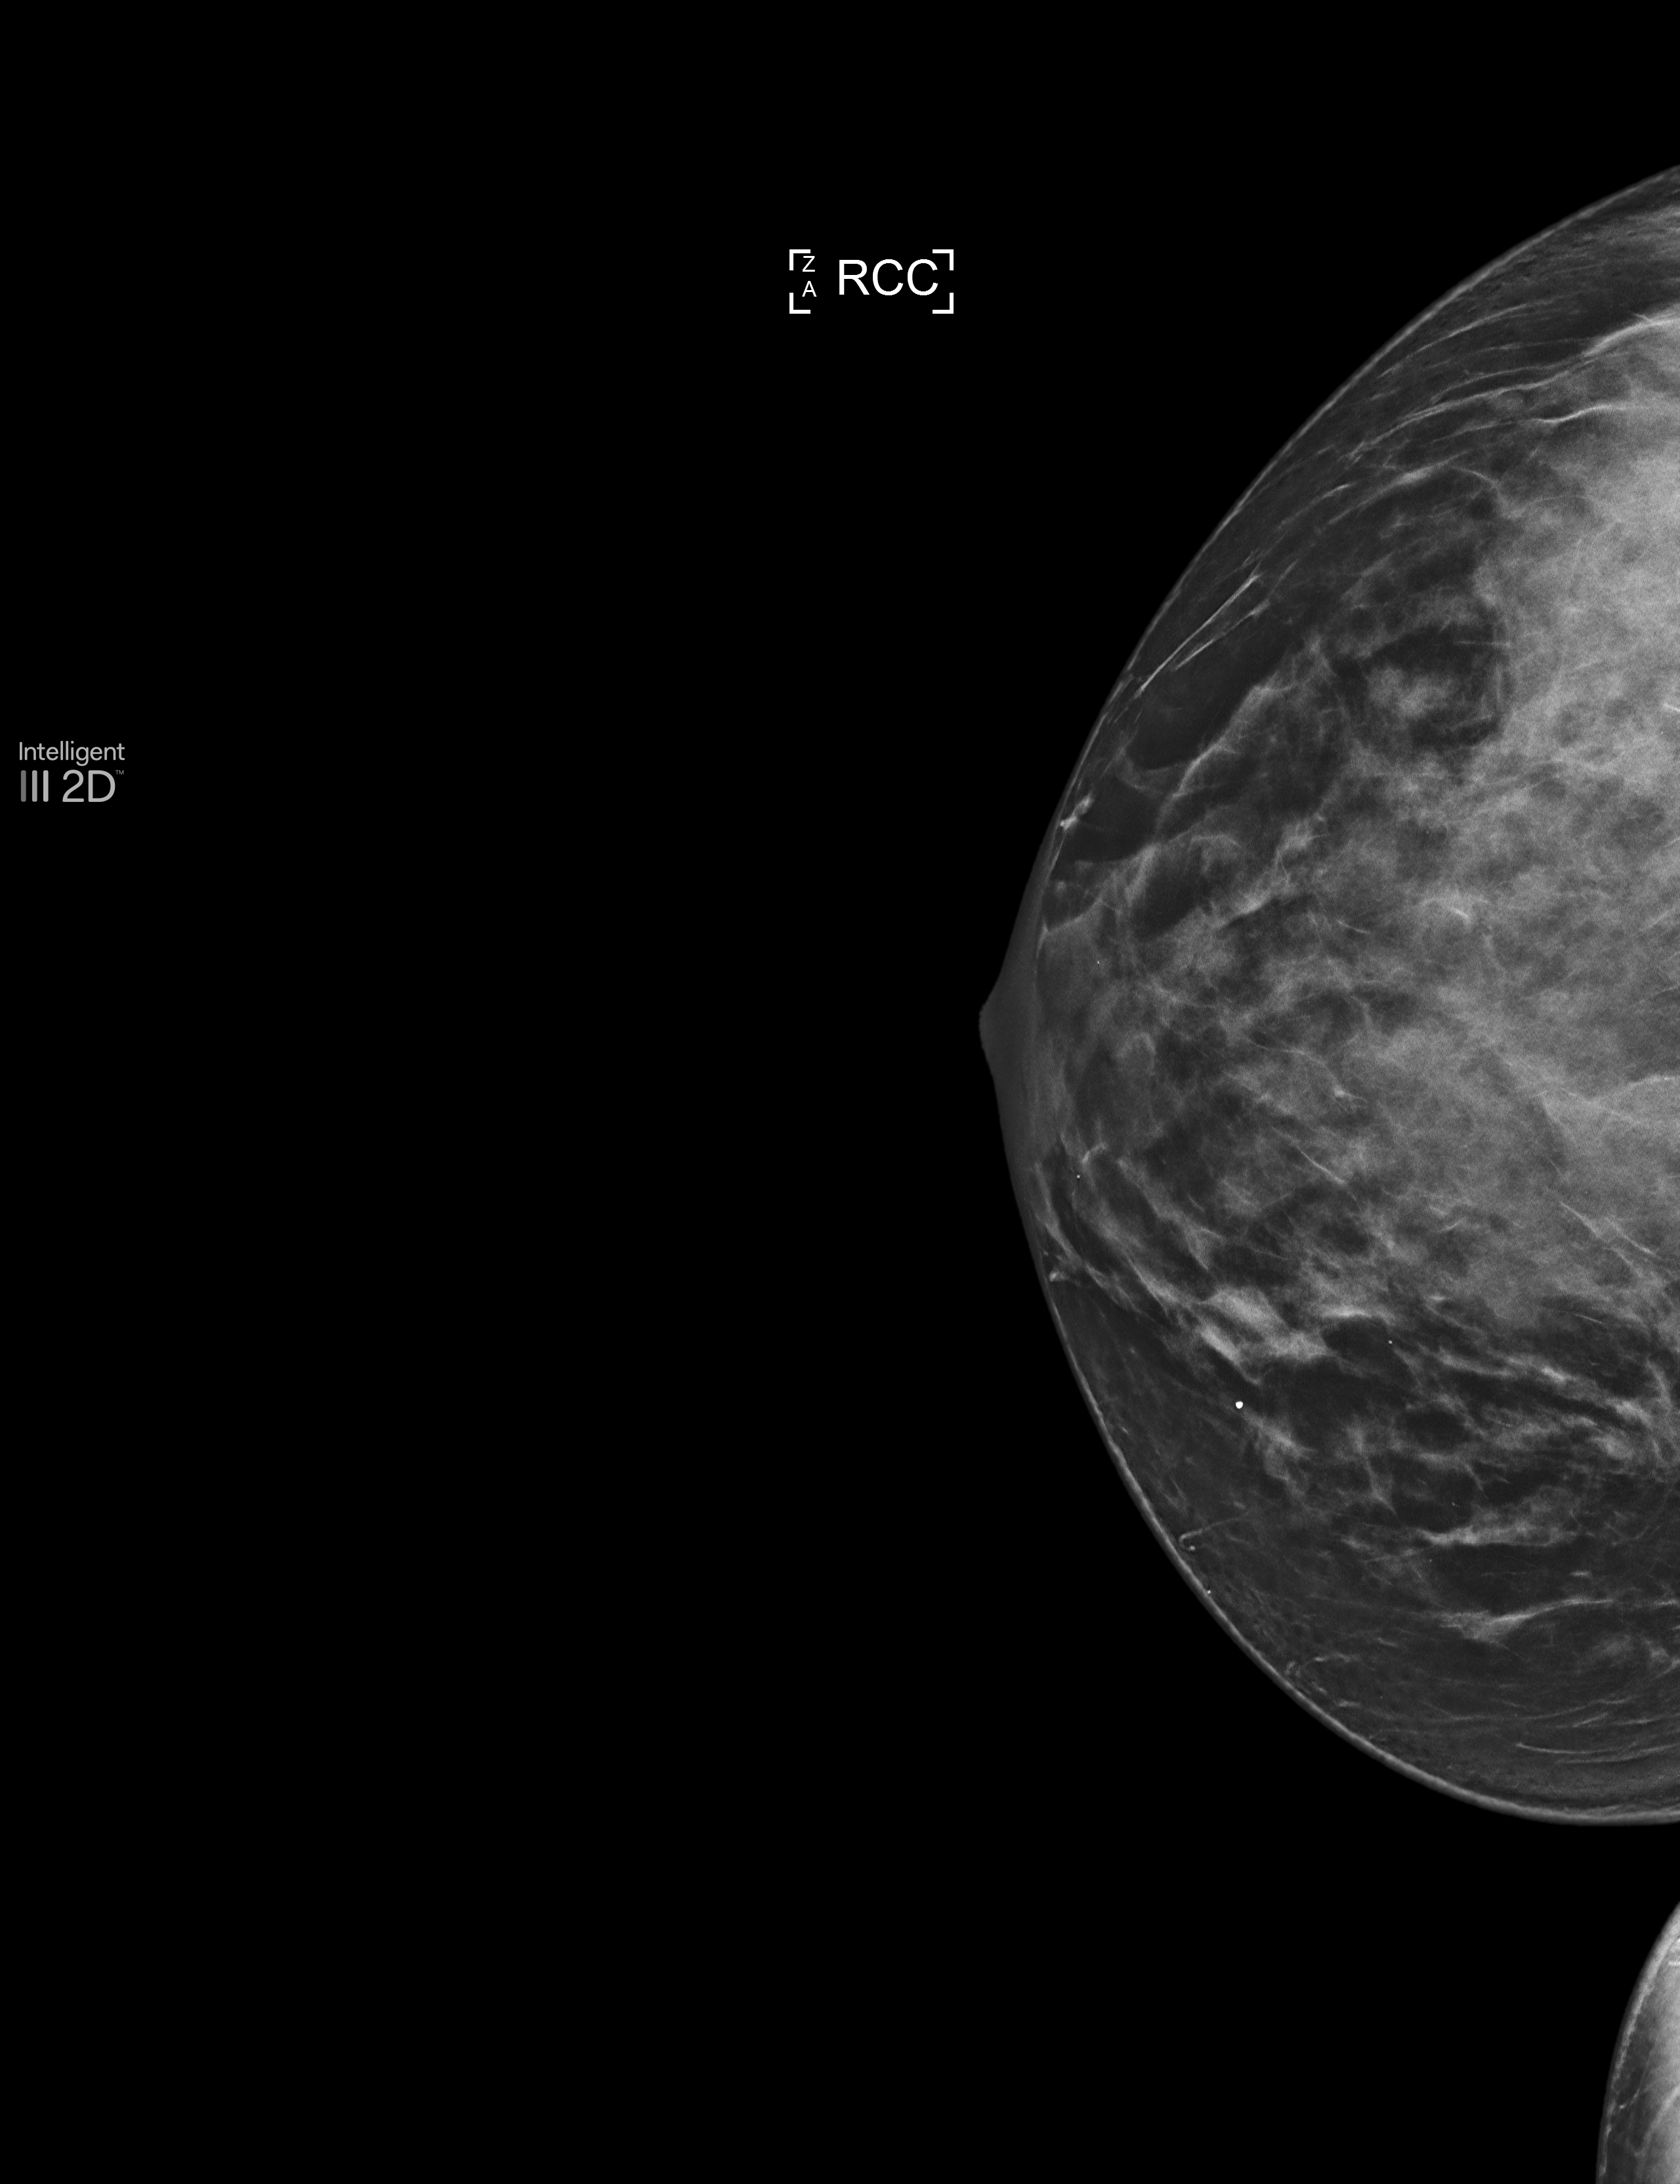
Annual screening mammography examination, system: Selenia Dimensions.
Image type: synthesized 2-D view from tomosynthesis. Breast: right. Projection: cranio-caudal projection.